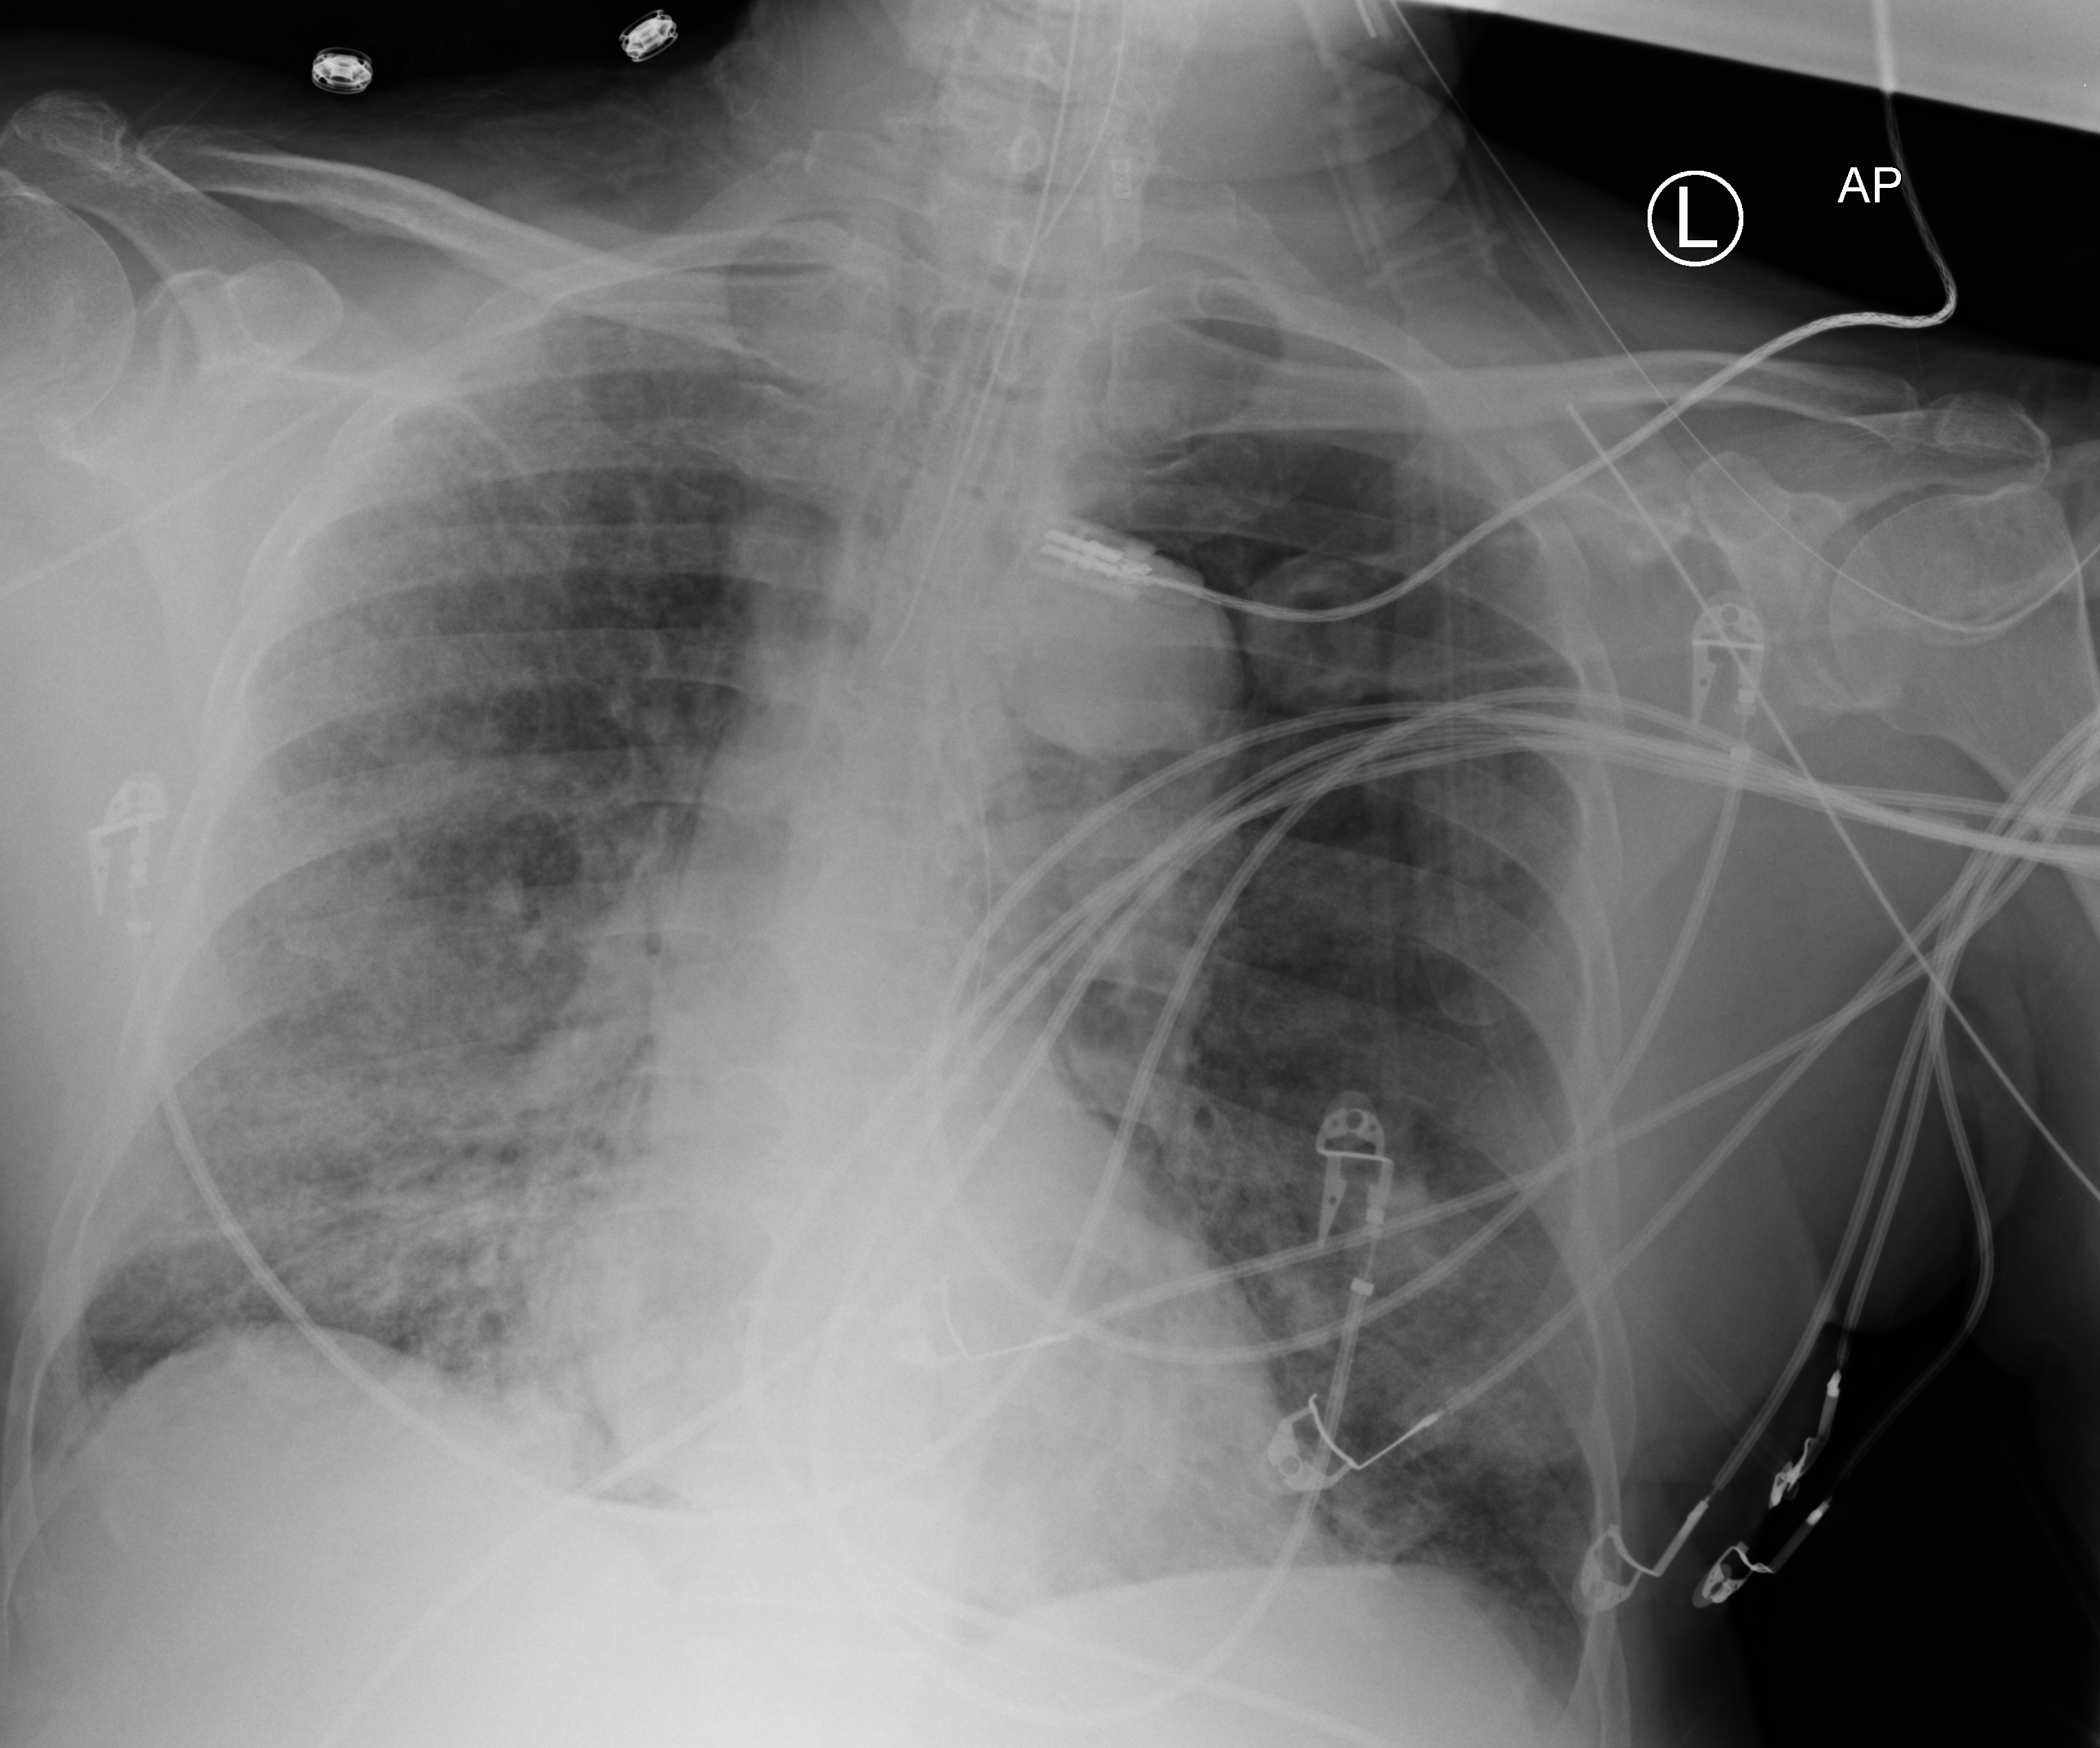
Portable chest radiograph, anteroposterior (AP) projection. Patient hospitalised with COVID-19; male, aged 60–74 years.
From the hospital-stay record, not from the radiograph (when in the stay this image was taken is not recorded):
- mechanically ventilated during this hospital stay: yes
- length of hospital stay: 10 days